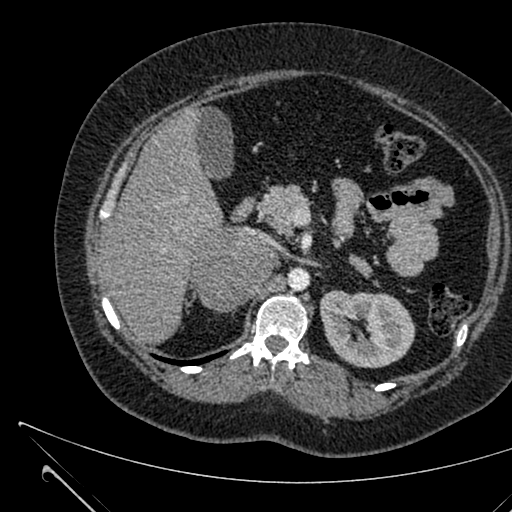
Contrast-enhanced abdominal CT, one axial slice. 120 kVp. Intravenous contrast given. Soft-tissue window (W 400 / L 40 HU). 1 mm slice thickness. 512 × 512 image matrix. Female patient, age 36 years. From the clinical record (not read from this slice): diagnosis: adrenocortical carcinoma; tumour side: right adrenal; tumour size at pathology: 10 cm; Ki-67 index: 20 %; stage (as recorded): 4.
Structures marked on this image (semi-automatic segmentation, software-assisted and operator-edited):
- mass: bounding box [x1, y1, x2, y2] px = [195, 228, 275, 312]